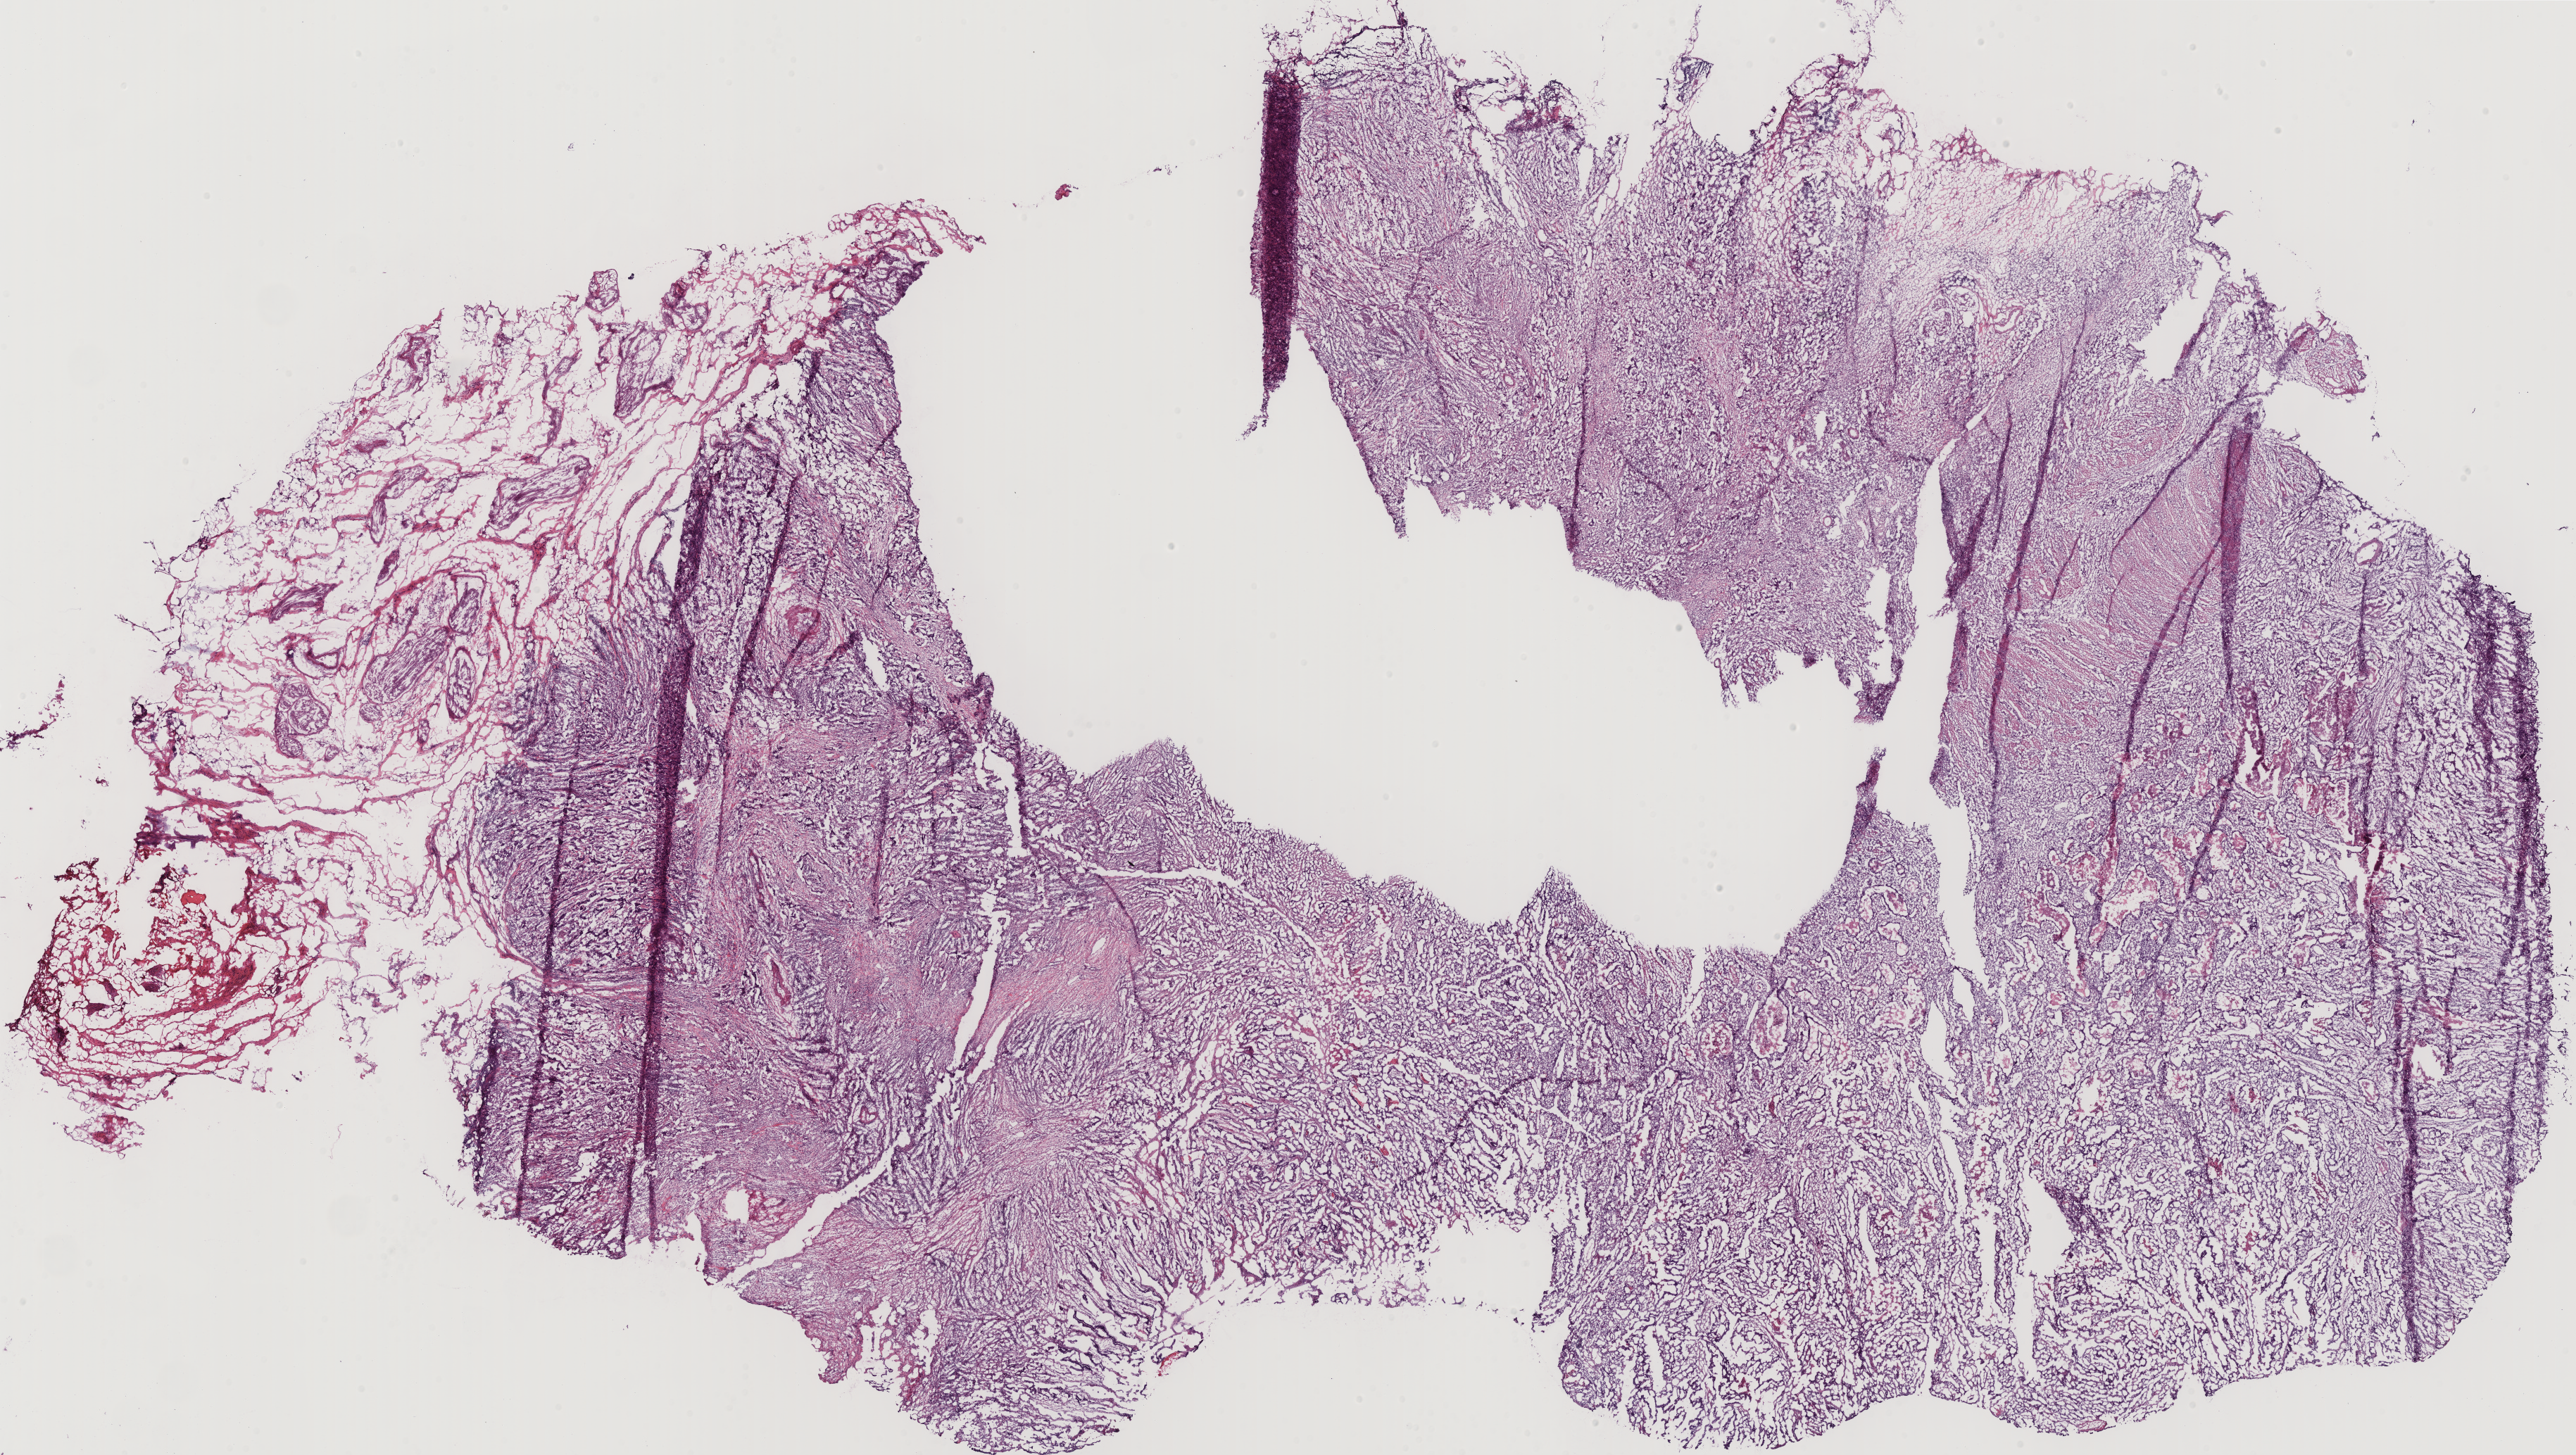
Digitized Hematoxylin and eosin (H&E) stained tissue section (whole slide) — shown as a low-resolution overview of the whole scanned area (about 28.8 x 16.3 mm, slide scanned at 40x); frozen section; stomach, primary tumour sample. Female, age 54 years at initial diagnosis. Histologic grade: G2 (moderately differentiated). Slide review estimates, as recorded: tumour cells 82%, tumour nuclei 65%, normal cells 2%, stromal cells 12%, necrosis 4%. Inflammatory infiltration, as recorded: lymphocyte infiltration 18%, monocyte infiltration 0%, neutrophil infiltration 0%.
Lymph nodes positive (case pathology): 10 of 10 examined. AJCC pathologic stage: IIIB. Pathologic diagnosis: Adenocarcinoma, NOS (cardia, NOS).